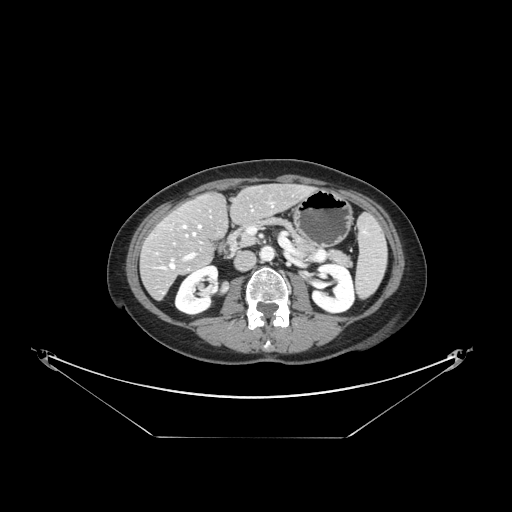
Contrast-enhanced abdominal CT, one axial slice; slice 62 of 148 in the series (ordered by position); soft-tissue window (W 400 / L 40 HU); 2.5 mm slice thickness; 512 × 512 image matrix, field of view 500 × 500 mm. Female patient, age 73 years. Case-level facts recorded for this patient, not image findings: diagnosis: colorectal cancer liver metastases, imaged before liver resection.
Outlined on this slice (outlined manually by an expert reader):
- hepatic veins: bounding box <162,204,273,269> (left, top, right, bottom; pixels)
- liver: <142,185,311,298>
- planned liver remnant (the part of the liver to remain after resection): <166,185,310,250>
- portal vein (with intrahepatic branches): <185,253,194,259>